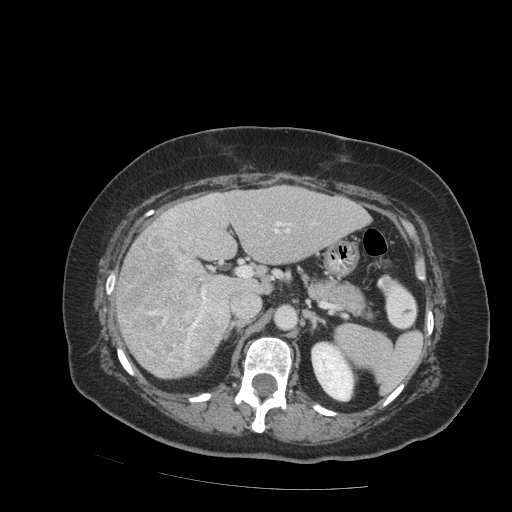
Contrast-enhanced abdominal CT (liver protocol), one axial slice. Slice 47 of 99 in the series (ordered by position). Reconstruction kernel STANDARD. 140 kVp. Soft-tissue window (W 400 / L 40 HU). 2.5 mm slice thickness. 512 × 512 image matrix, field of view 400 × 400 mm. Case-level facts recorded for this patient, not image findings: diagnosis: hepatocellular carcinoma (patient treated with transarterial chemoembolisation; whether this scan precedes or follows treatment is not stated here); TNM stage (as recorded): Stage-IVB; Child-Pugh class: A.
Structures marked on this image (semi-automatically segmented with operator editing):
- liver parenchyma outside the tumour (the mass and vessels are separate outlines, so this box may not span the whole liver): bounding box [x1, y1, x2, y2] px = [116, 186, 370, 378]
- mass: [117, 236, 227, 375]
- liver vessels: [165, 213, 290, 278]